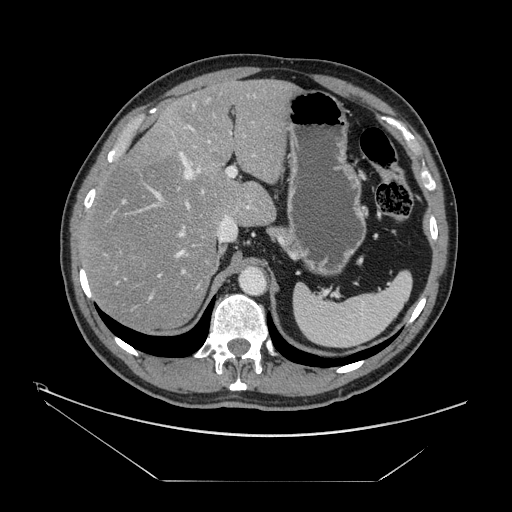
Contrast-enhanced abdominal CT, one axial slice; position 102 of 161 along the scan axis; 120 kVp; soft-tissue window (W 400 / L 40 HU); 2.5 mm slice thickness; 512 × 512 image matrix, field of view 440 × 440 mm. Male patient, age 65 years. From the clinical record (not read from this slice): diagnosis: colorectal cancer liver metastases, imaged before liver resection; multiple liver metastases: yes; largest metastasis: 4.2 cm; chemotherapy before resection: yes.
Annotated regions visible in this slice (outlined manually by an expert reader):
- hepatic veins: bounding box (x1, y1, x2, y2) in pixels: (117, 126, 210, 283)
- liver: (82, 81, 294, 329)
- planned liver remnant (the part of the liver to remain after resection): (81, 80, 294, 329)
- portal vein (with intrahepatic branches): (113, 94, 256, 309)